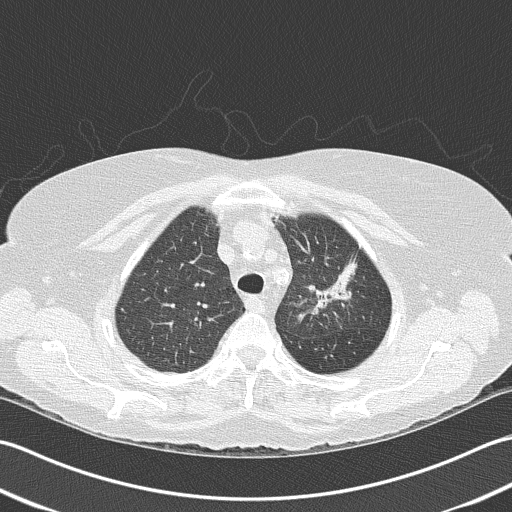
Chest CT (low-dose screening protocol), one axial image. First (baseline) screen. Lung window (W 1500 / L -600 HU). Slice 127 of 159 in the series. 512 × 512 image matrix, field of view 350 × 350 mm. Female, age 68 years at enrolment.
• Lesion marked by an expert reader, box from (x=294, y=242) to (x=368, y=320) px.
• Screening reader's record for this exam: no non-calcified nodule ≥4 mm recorded.
• Official screen result: negative screen, minor abnormalities not suspicious for lung cancer.
• Participant outcome: lung cancer diagnosed 763 days after this screen (after the third annual screen) — adenocarcinoma, NOS, left upper lobe, poorly differentiated (G3), stage IB (AJCC 6th edition), 50 mm at pathology.